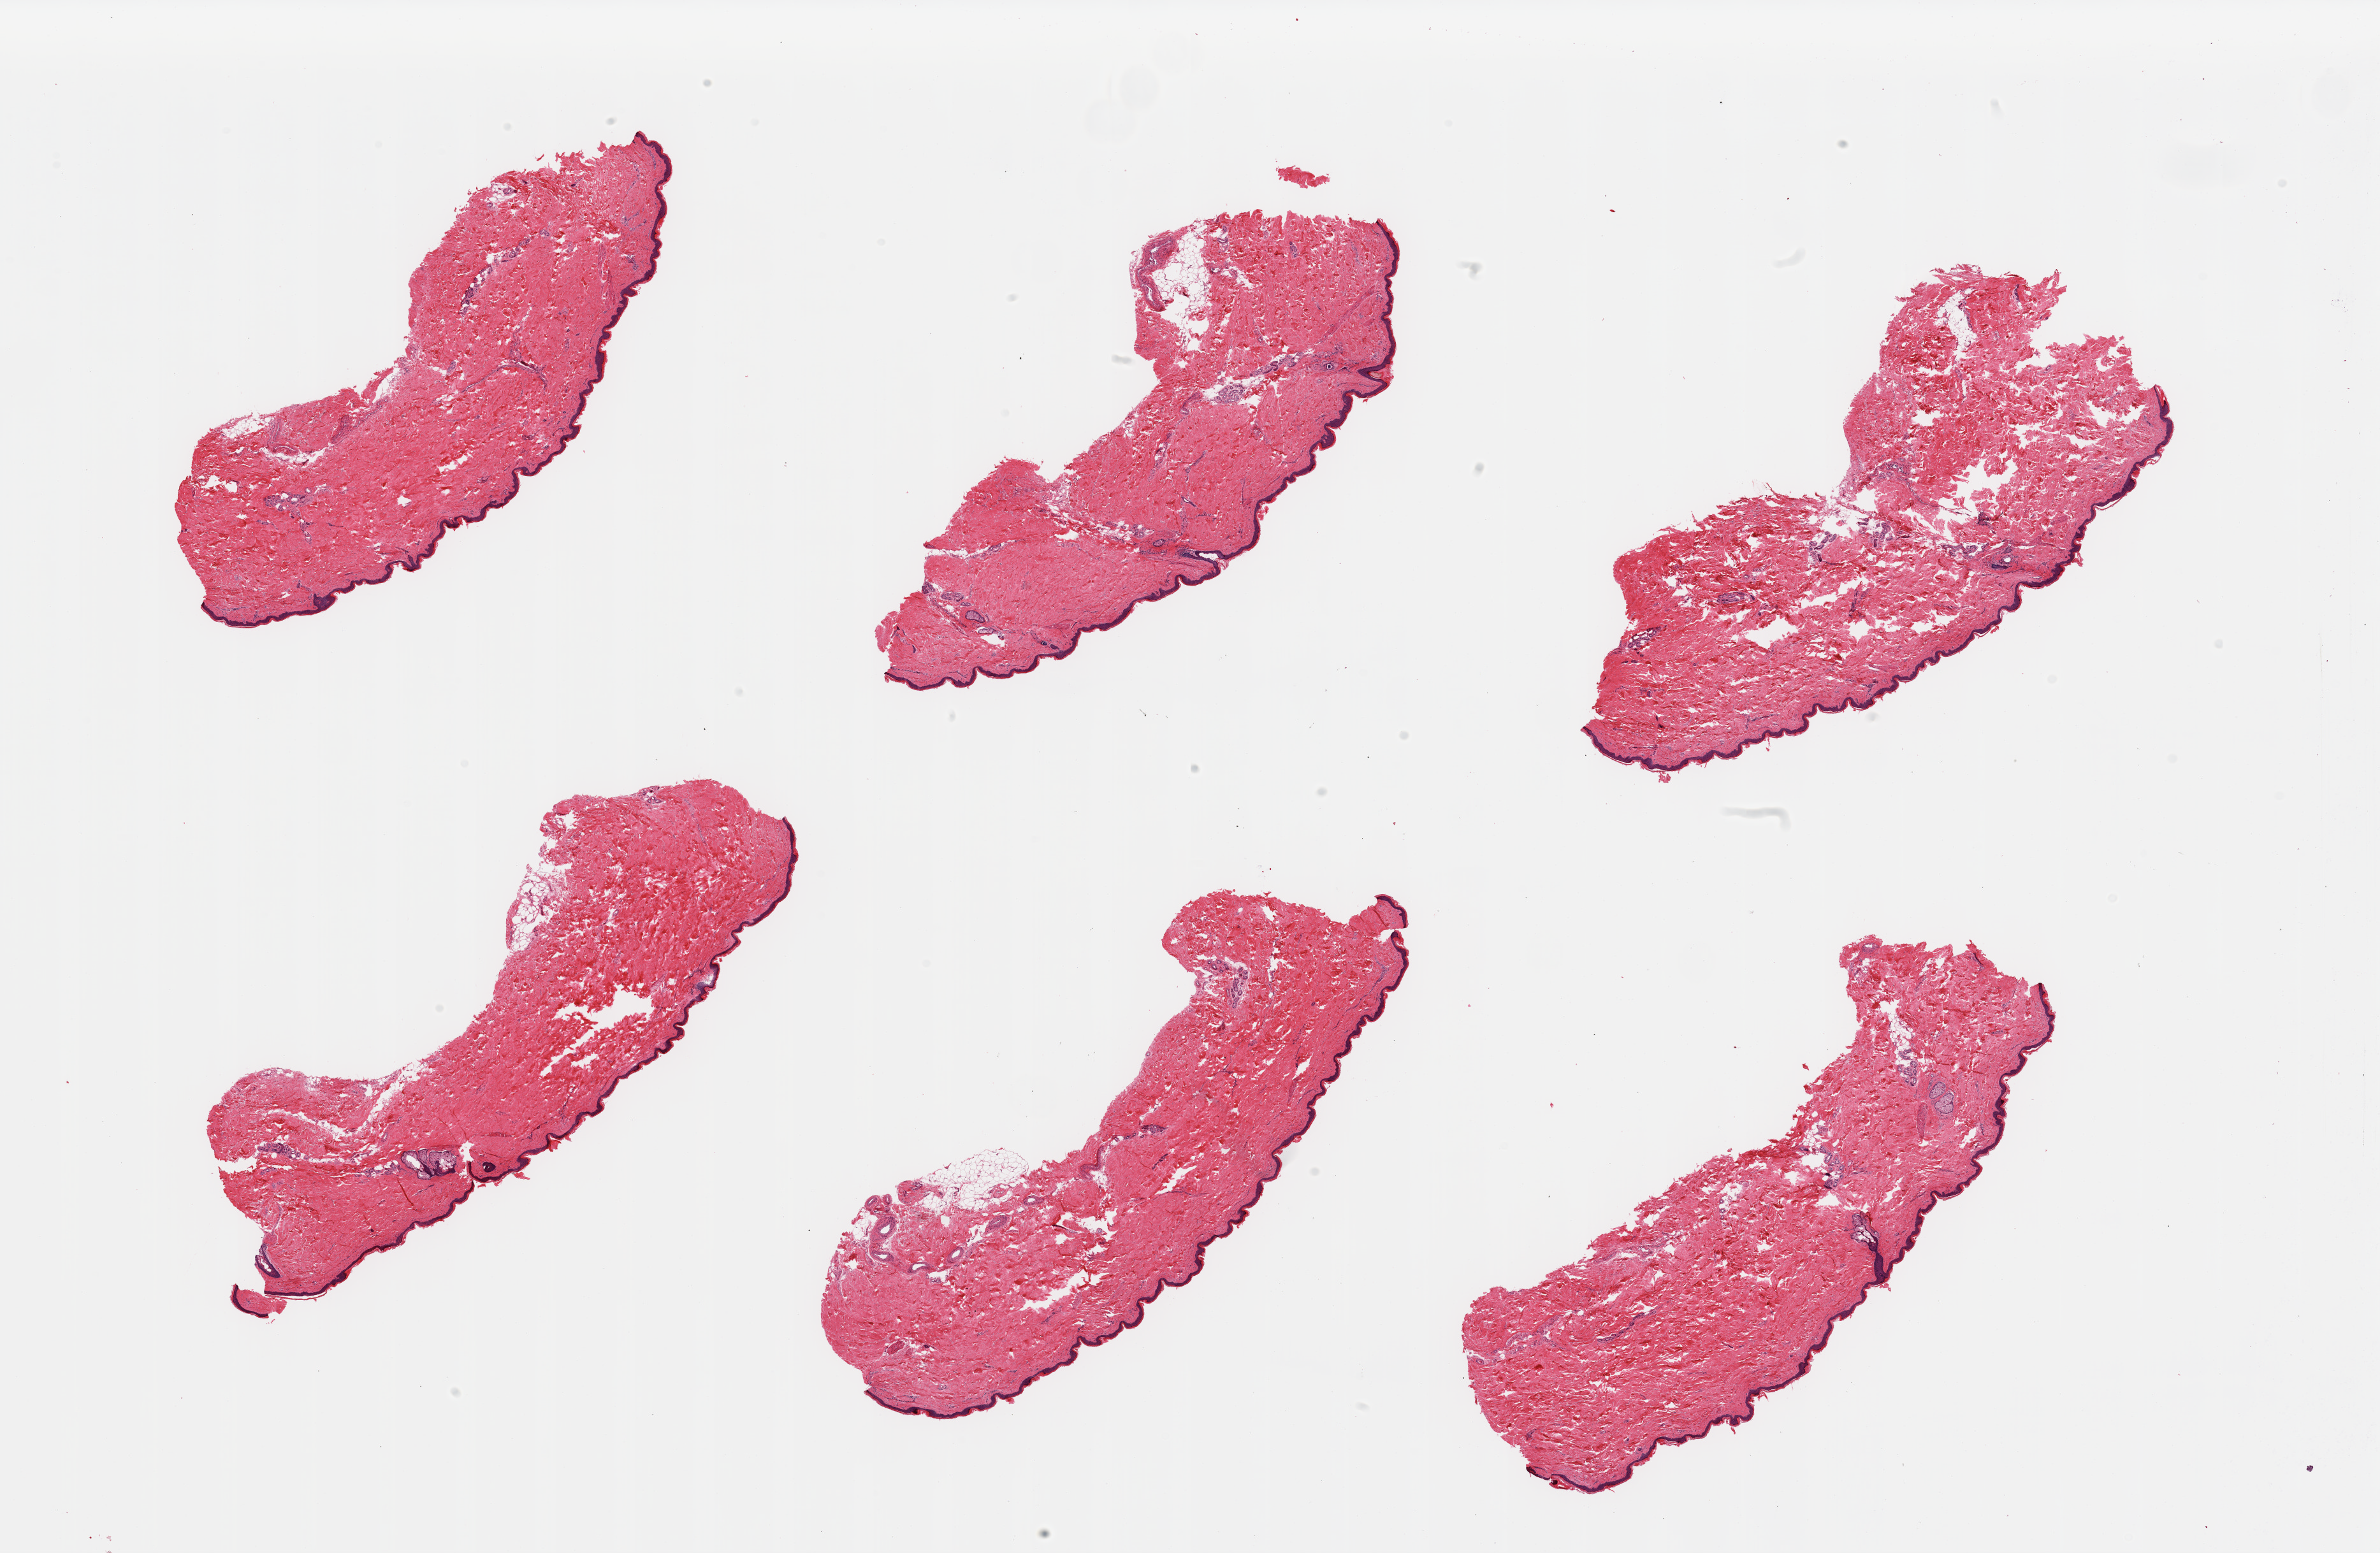
Haematoxylin and eosin whole-slide image, whole scanned area (about 29.5 x 19.3 mm) shown as a low-resolution overview; PAXgene-fixed, paraffin-embedded tissue; section of skin of lower leg (target tissue); tissue donor sample.
Review note (as recorded): 6 pieces; well trimmed; minimal dermal fat.